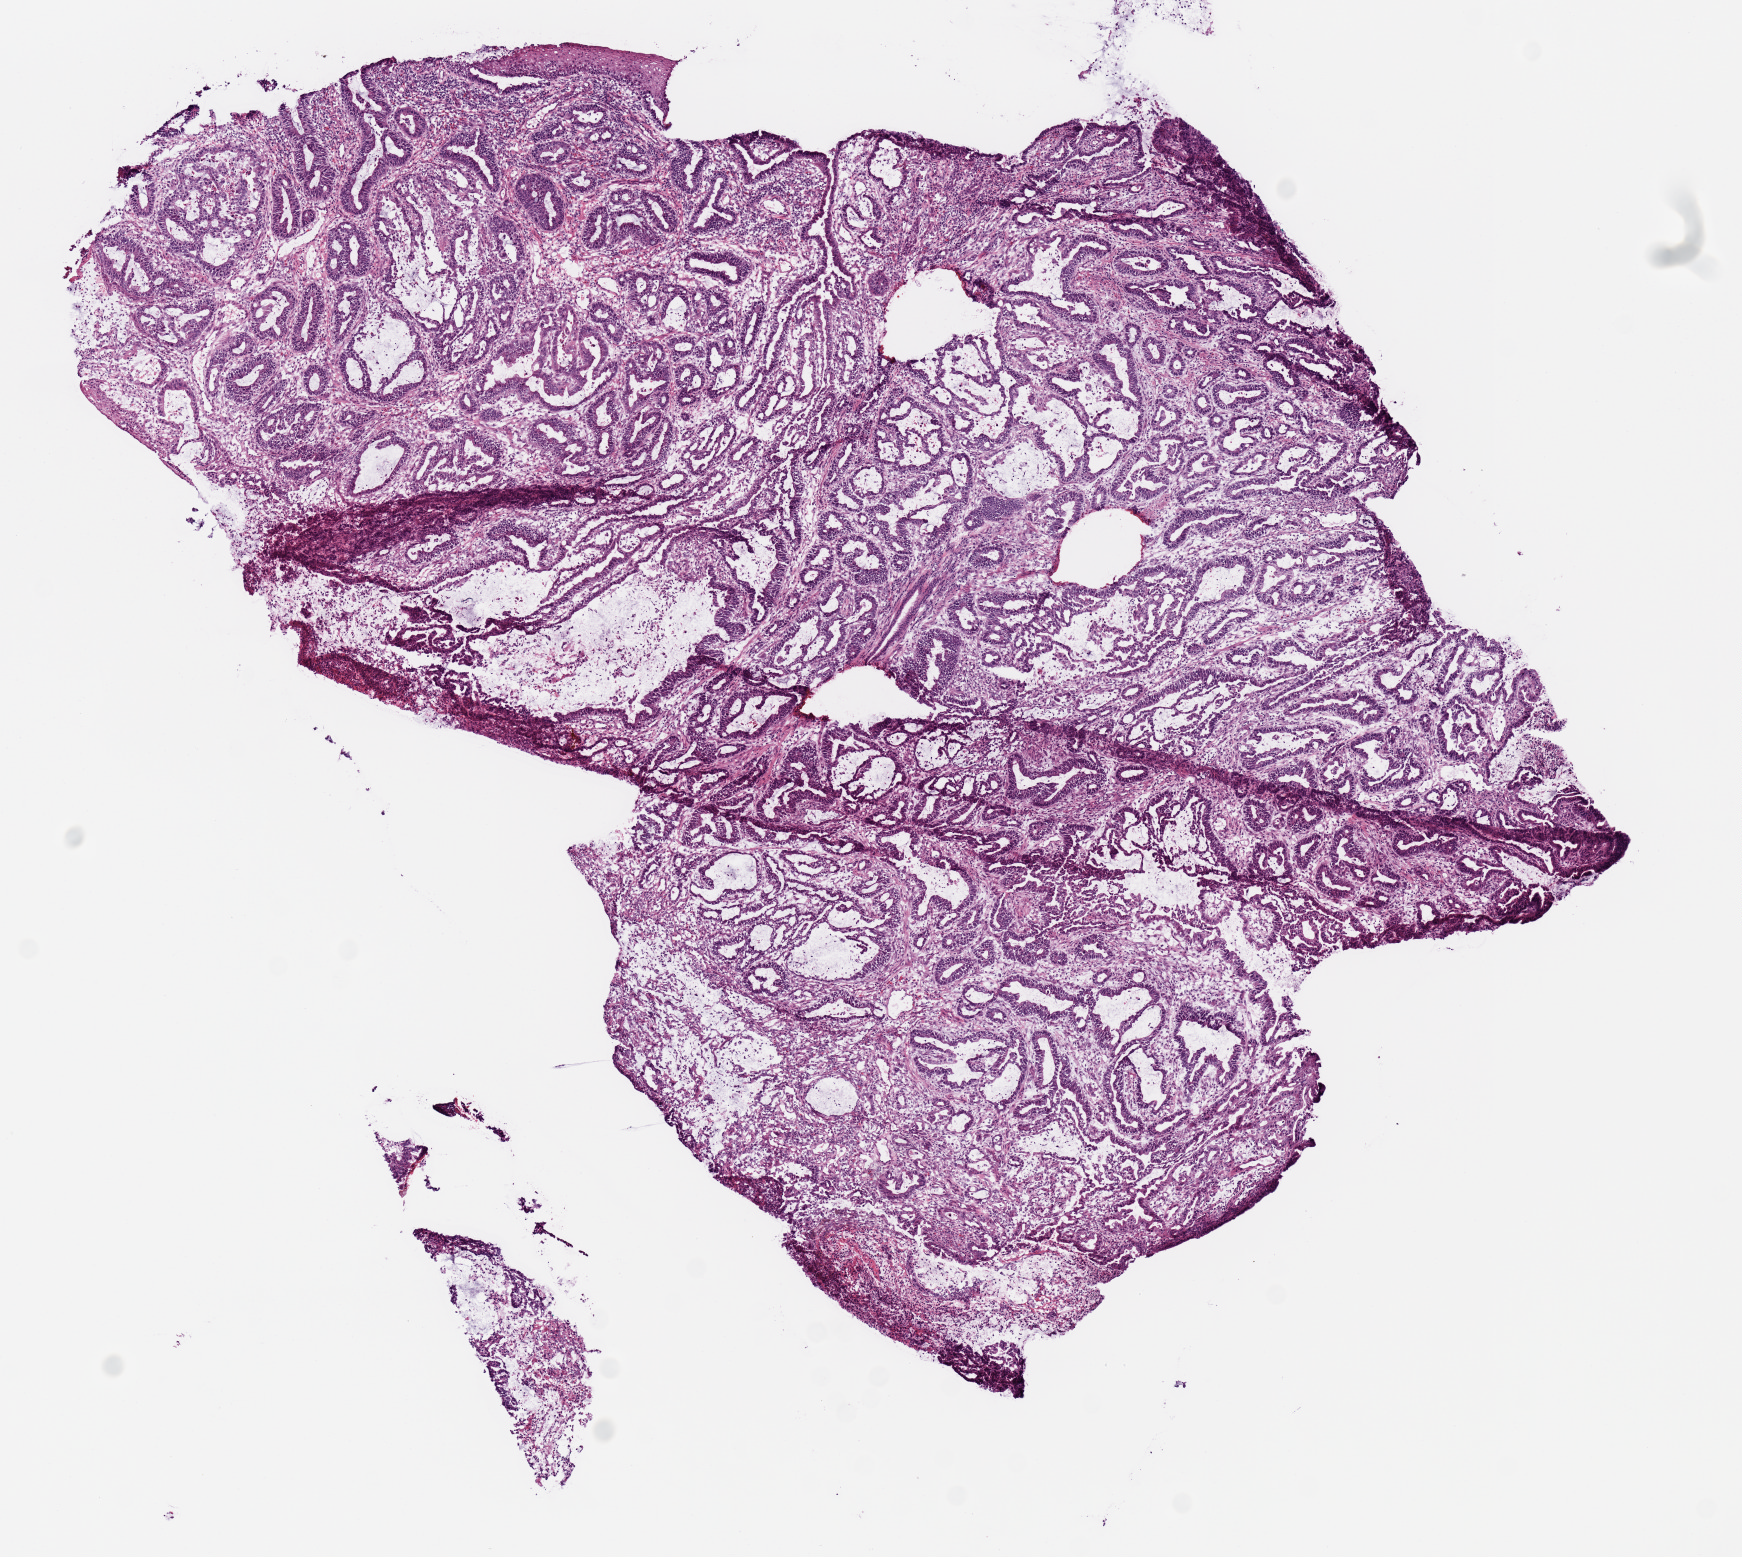
H&E-stained whole-slide image — shown as a low-resolution overview of the whole scanned area (about 6.9 x 6.2 mm, slide scanned at 20x). Frozen section from the top of the tissue portion. Sample: primary tumour, stomach. Male patient; age at initial diagnosis 69 years.
Histologic diagnosis: Mucinous adenocarcinoma (cardia, NOS).